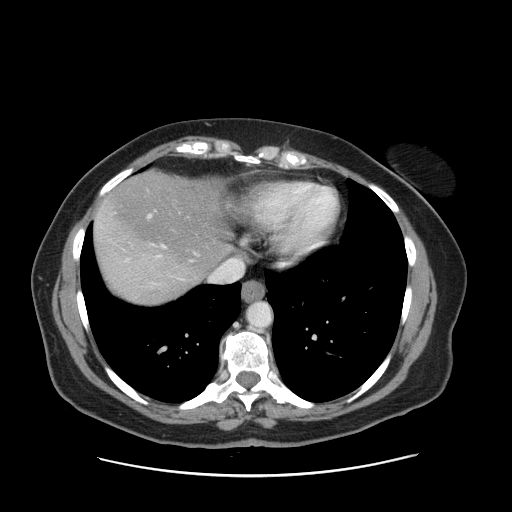
Contrast-enhanced abdominal CT, one axial slice; slice 138 of 161 in the series (ordered by position); 120 kVp; intravenous contrast given; soft-tissue window (W 400 / L 40 HU); 2.5 mm slice thickness; 512 × 512 image matrix. Female patient, age 62 years. Case-level facts recorded for this patient, not image findings: diagnosis: colorectal cancer liver metastases, imaged before liver resection; multiple liver metastases: no; largest metastasis: 2.5 cm; disease in both lobes: no.
Structures marked on this image (manually delineated by an expert):
- hepatic veins: bounding box <126,188,243,282> (left, top, right, bottom; pixels)
- liver: <95,173,228,304>
- planned liver remnant (the part of the liver to remain after resection): <98,173,228,275>
- portal vein (with intrahepatic branches): <149,214,151,217>